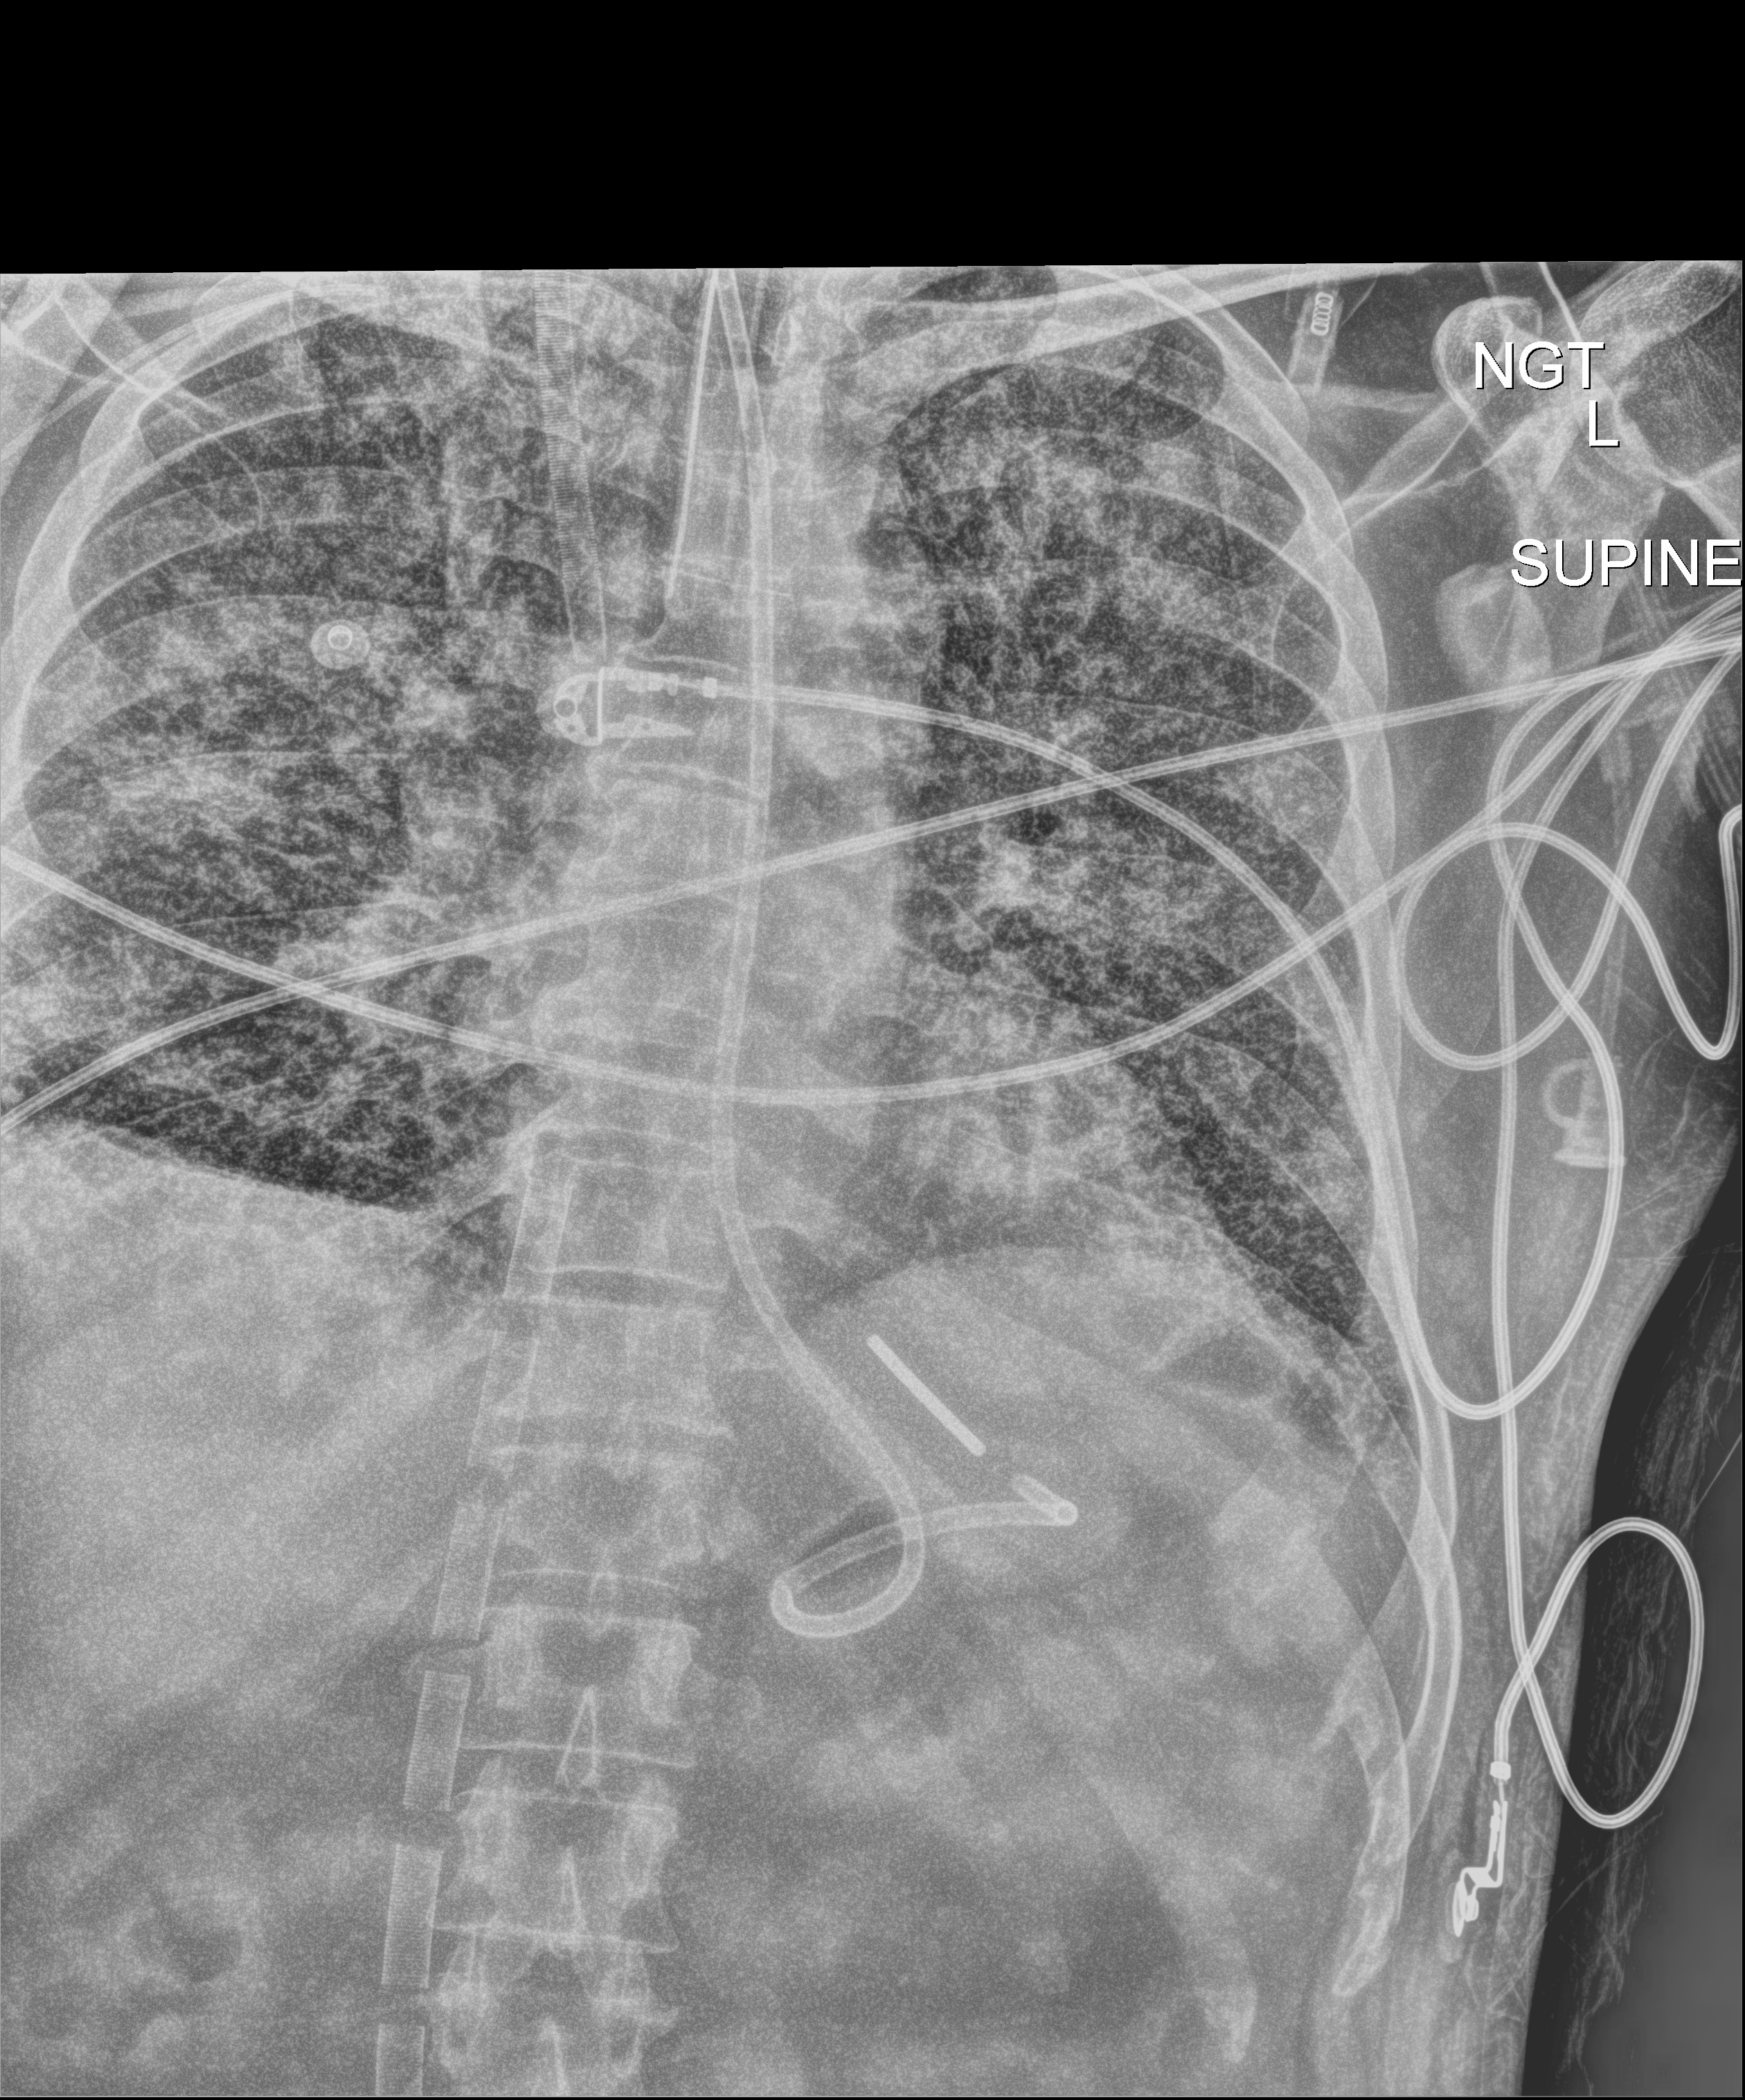
Bedside chest radiograph (digital radiography). Patient hospitalised with COVID-19; male, aged 18–59 years.
From the hospital-stay record, not from the radiograph (when in the stay this image was taken is not recorded):
- COPD (admission record): no